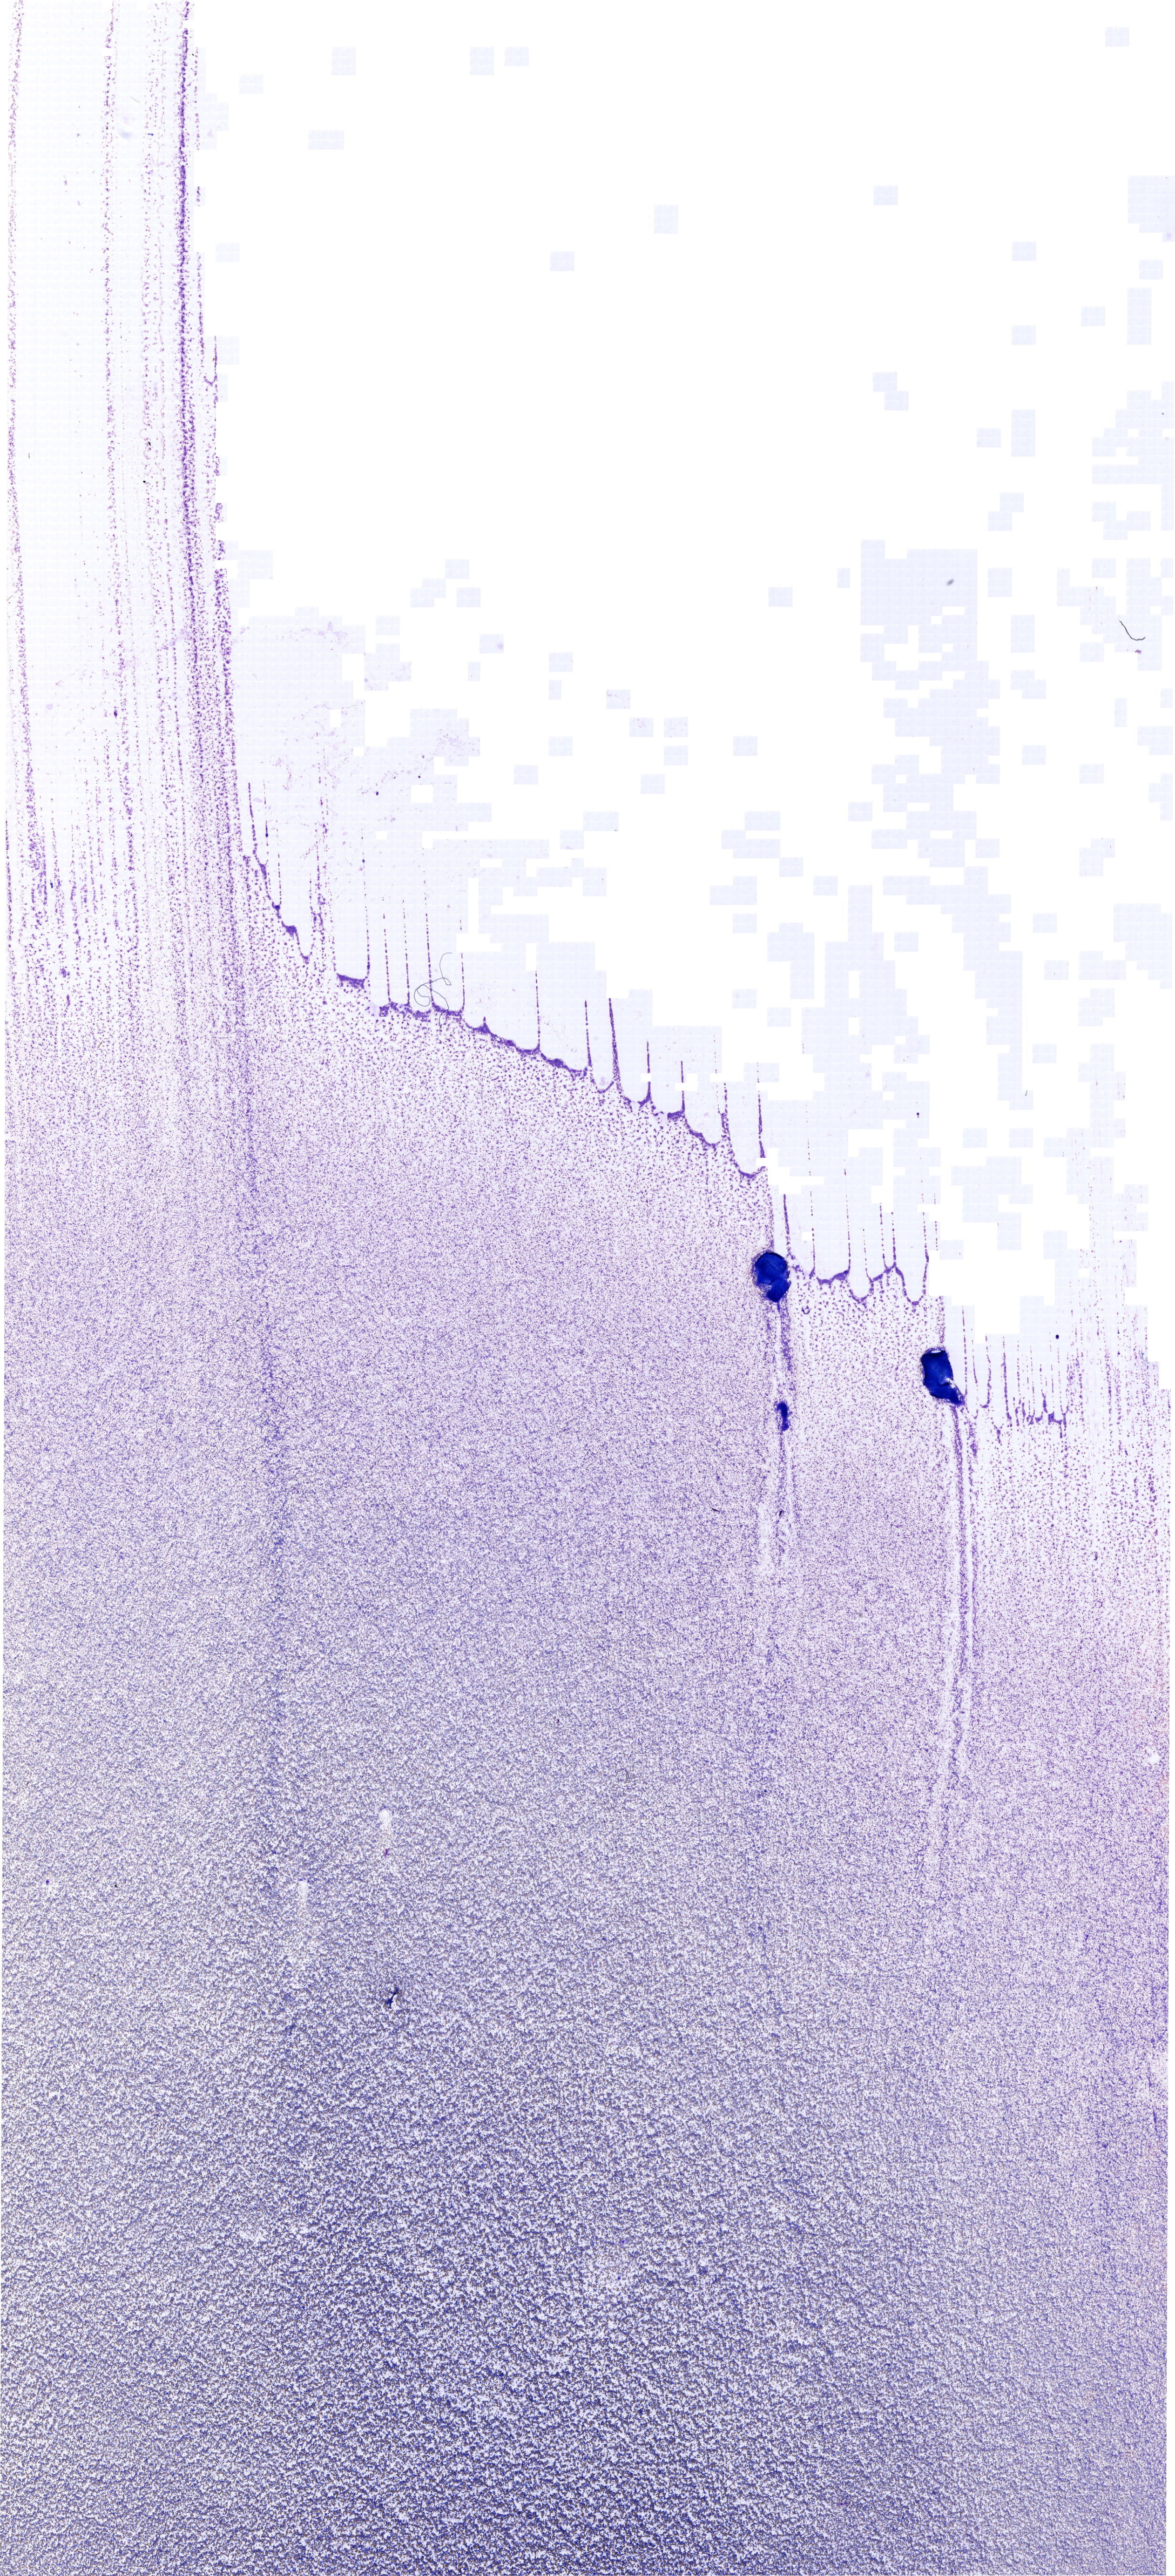
Whole-slide image of a May-Grünwald–Giemsa-stained bone marrow aspirate smear — a low-resolution overview of the entire scanned area, about 19.7 x 43.2 mm. Patient sex: female.
Diagnosis: Mixed Phenotype Acute Leukemia, B/Myeloid.